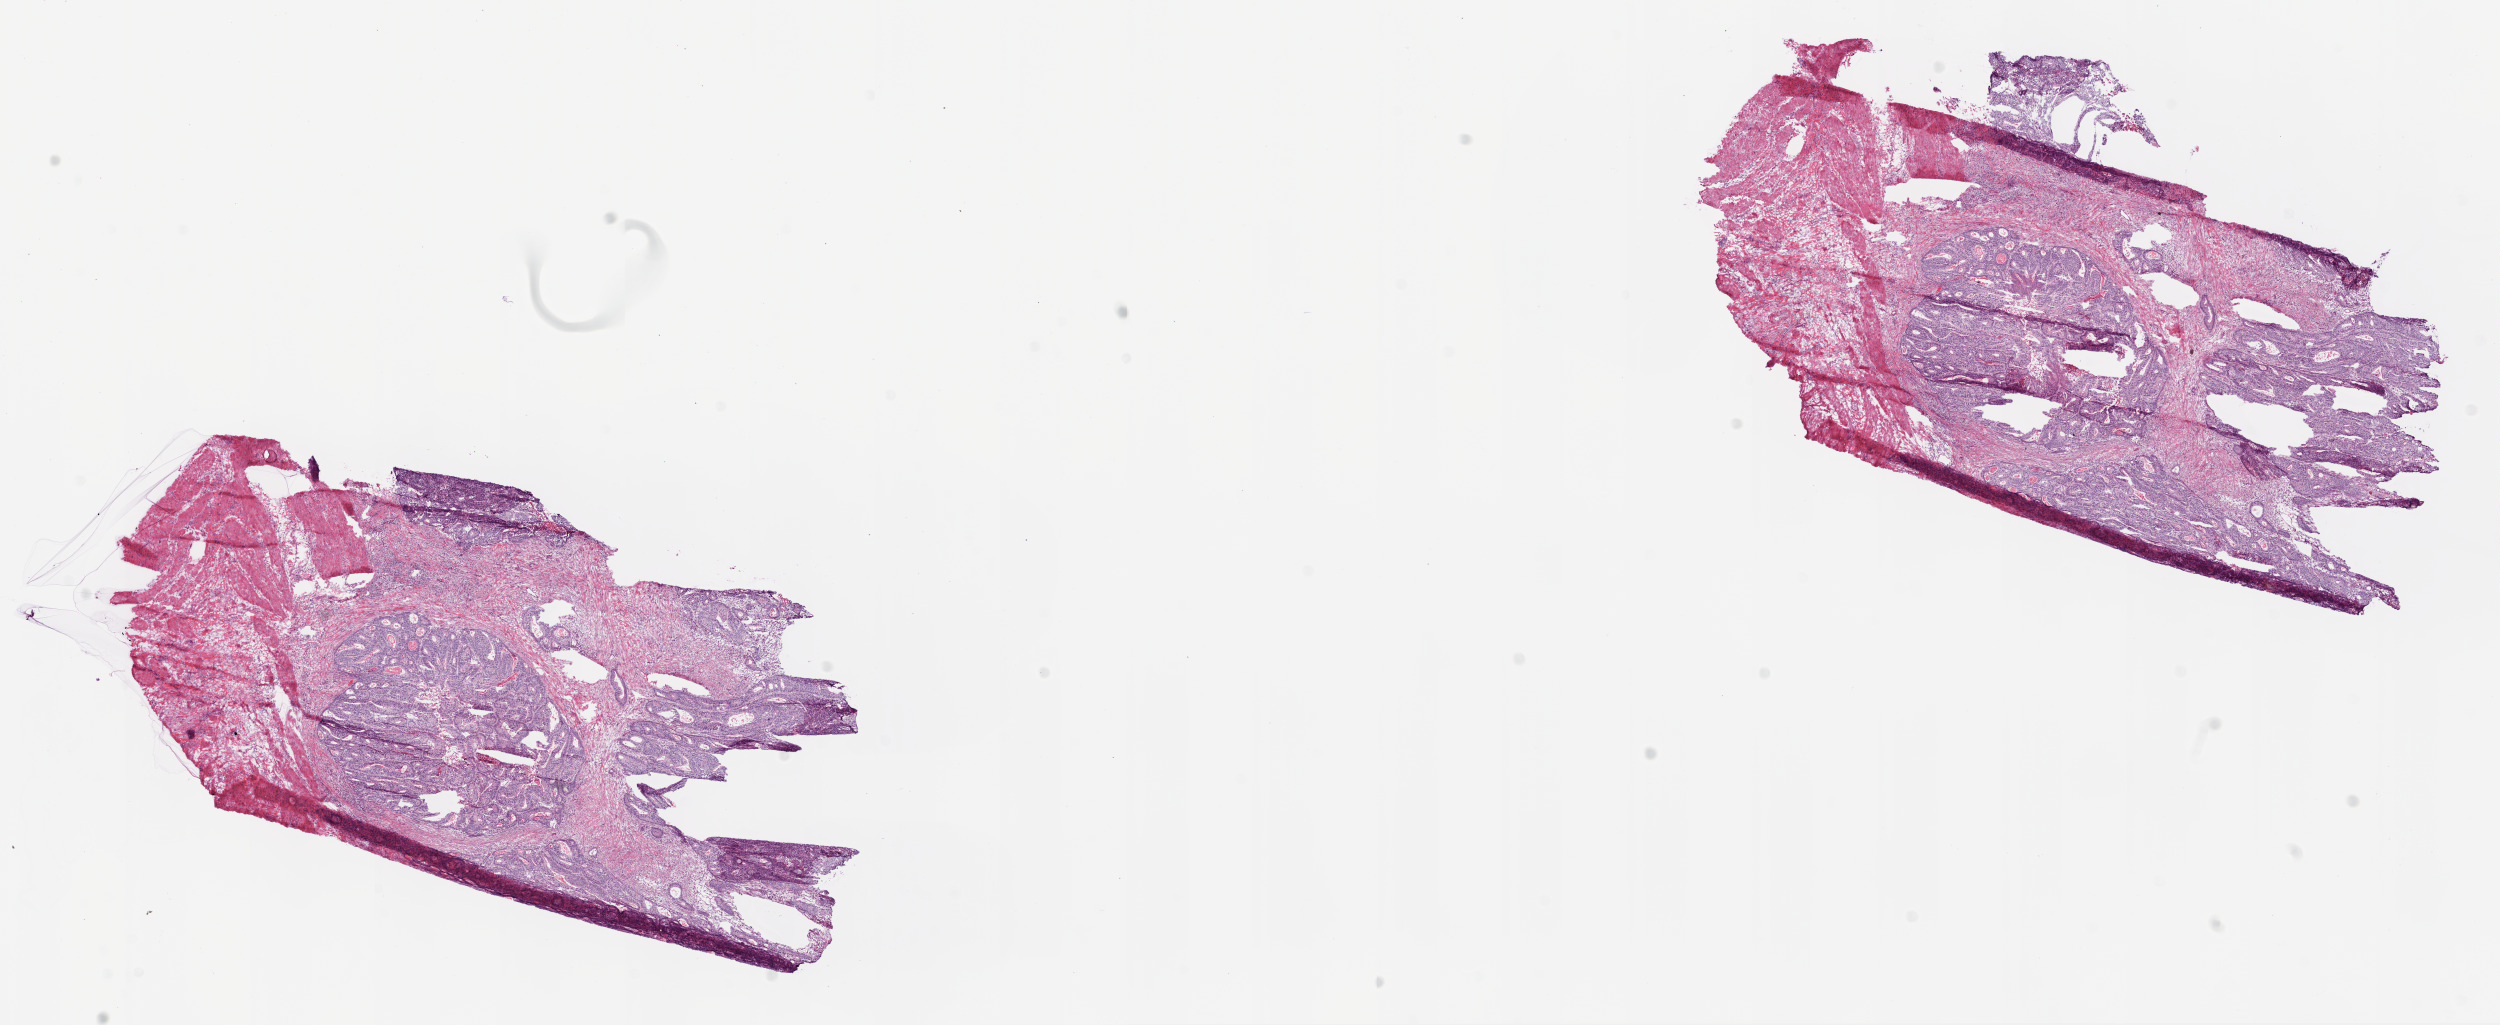
Digitized Hematoxylin and eosin (H&E) stained tissue section (whole slide) — whole scanned area (about 20.1 x 8.2 mm) shown as a low-resolution overview. Frozen section from the top of the tissue portion. Colon, primary tumour sample. Female patient; age at initial diagnosis 77 years. Slide review estimates, as recorded: tumour cells 50%, tumour nuclei 70%, normal cells 0%, stromal cells 50%, necrosis 0%.
- lymph nodes positive (case pathology): 0 of 36 examined
- pathologic diagnosis: Adenocarcinoma, NOS (ascending colon)
- AJCC pathologic stage: IIA